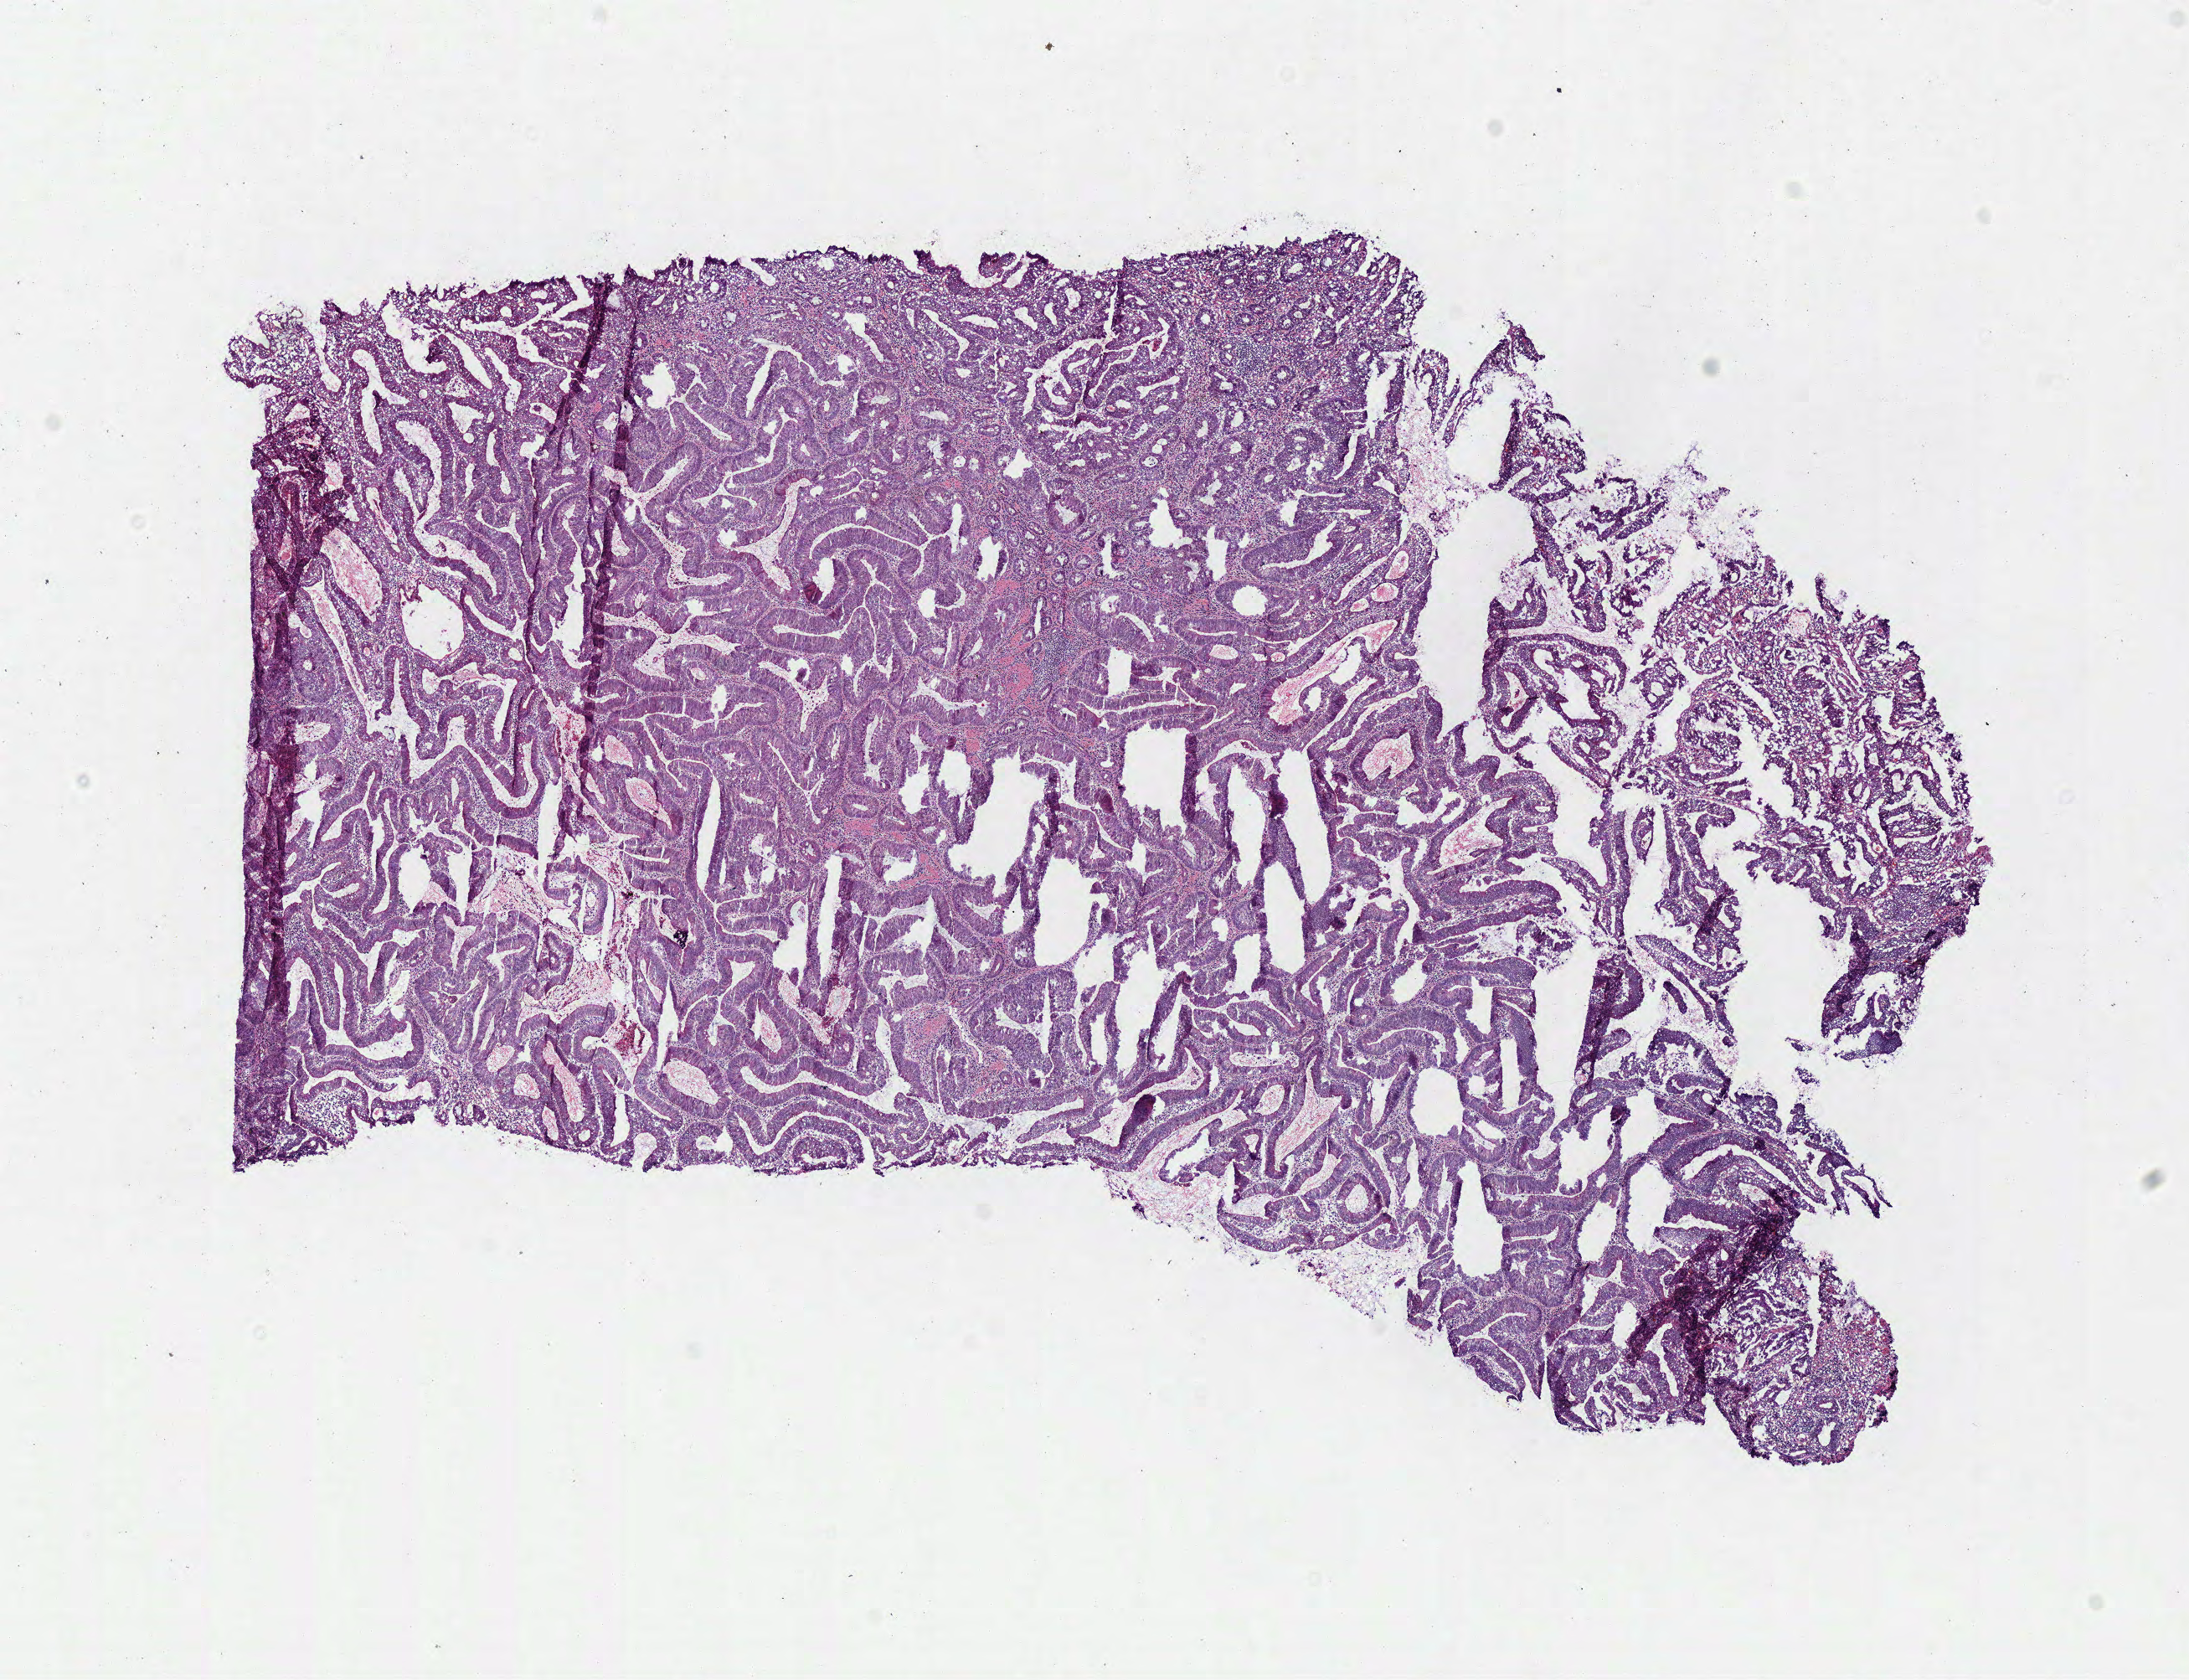
H&E-stained whole-slide image, low-resolution overview of the scanned area, about 10.3 x 7.9 mm, frozen section, primary tumour sample from the colon. Female, age 49 years at initial diagnosis. Composition of this section per pathologist review: tumour cells 90%, tumour nuclei 80%, normal cells 0%, stromal cells 10%, necrosis 0%.
Lymph nodes positive (case pathology): 1 of 26 examined. AJCC pathologic stage: III (5th edition). Pathologic diagnosis: Adenocarcinoma, NOS (transverse colon).